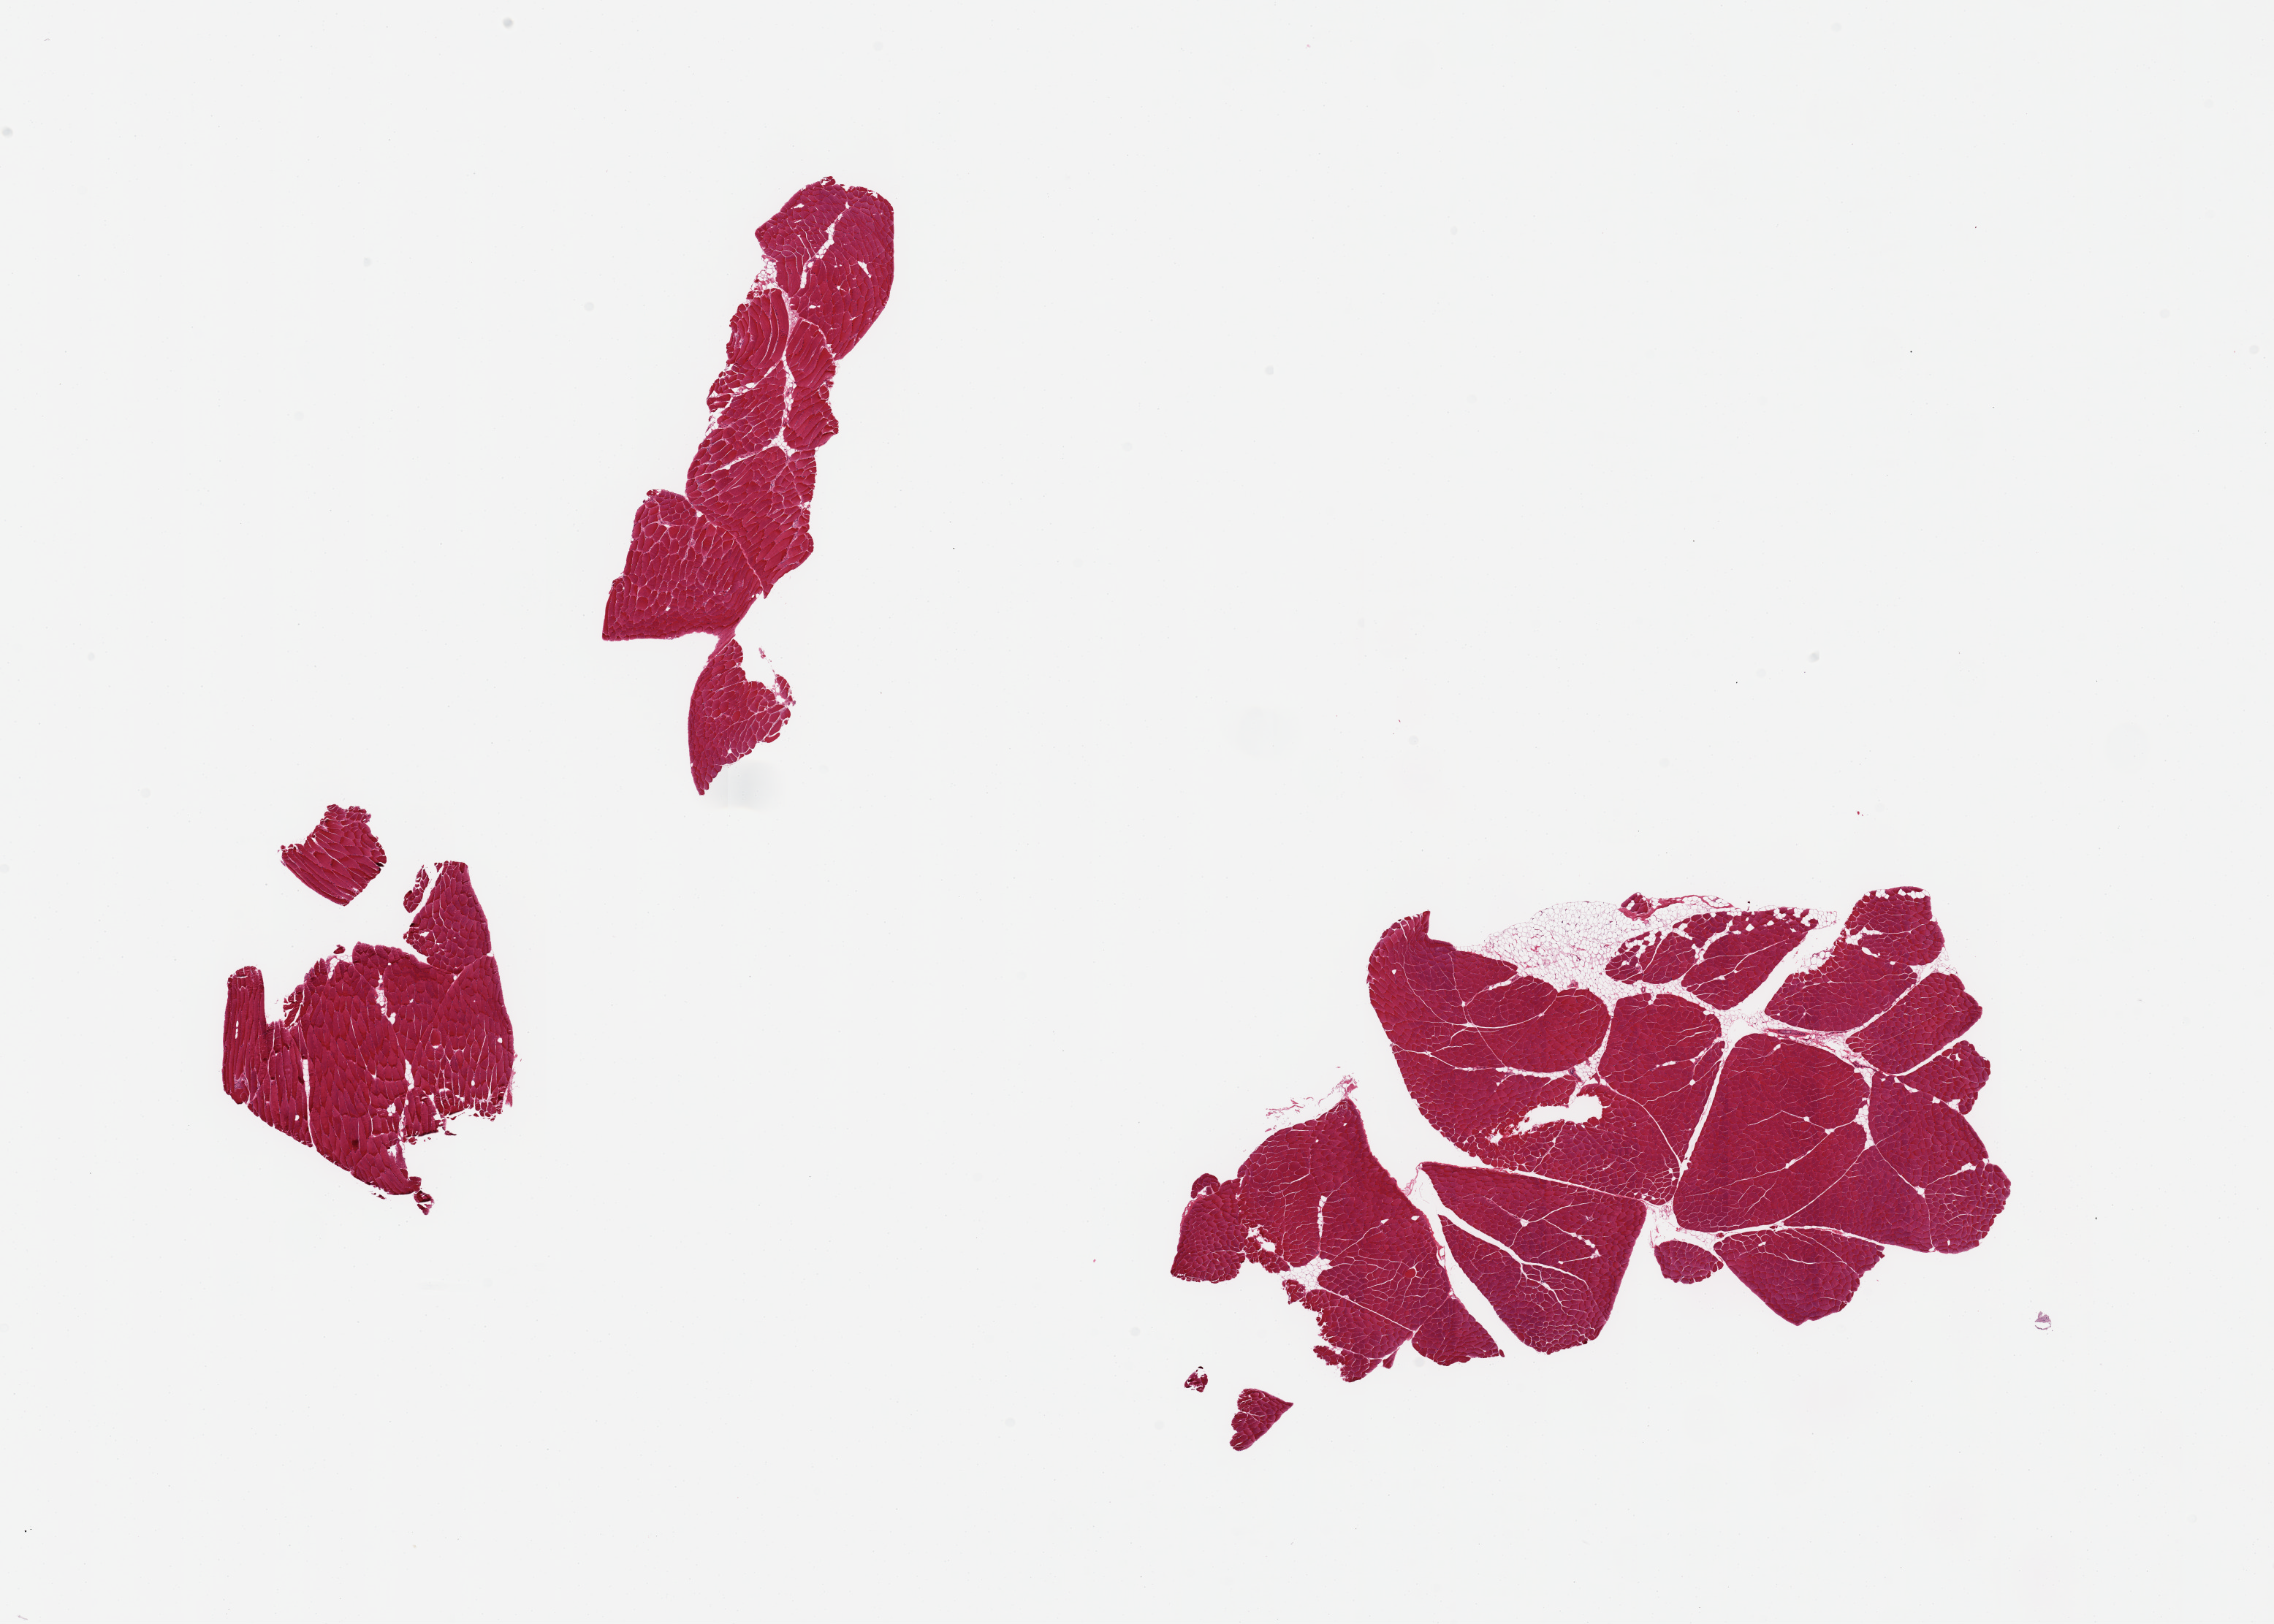
Digitized haematoxylin and eosin-stained section — low-resolution overview of the scanned area, about 24.6 x 17.6 mm, PAXgene-fixed, paraffin-embedded tissue, sampled site (target tissue): skeletal muscle, donor tissue sample. Female donor.
- reviewer comment on this tissue sample: 2 pieces, minimal interstitial fat